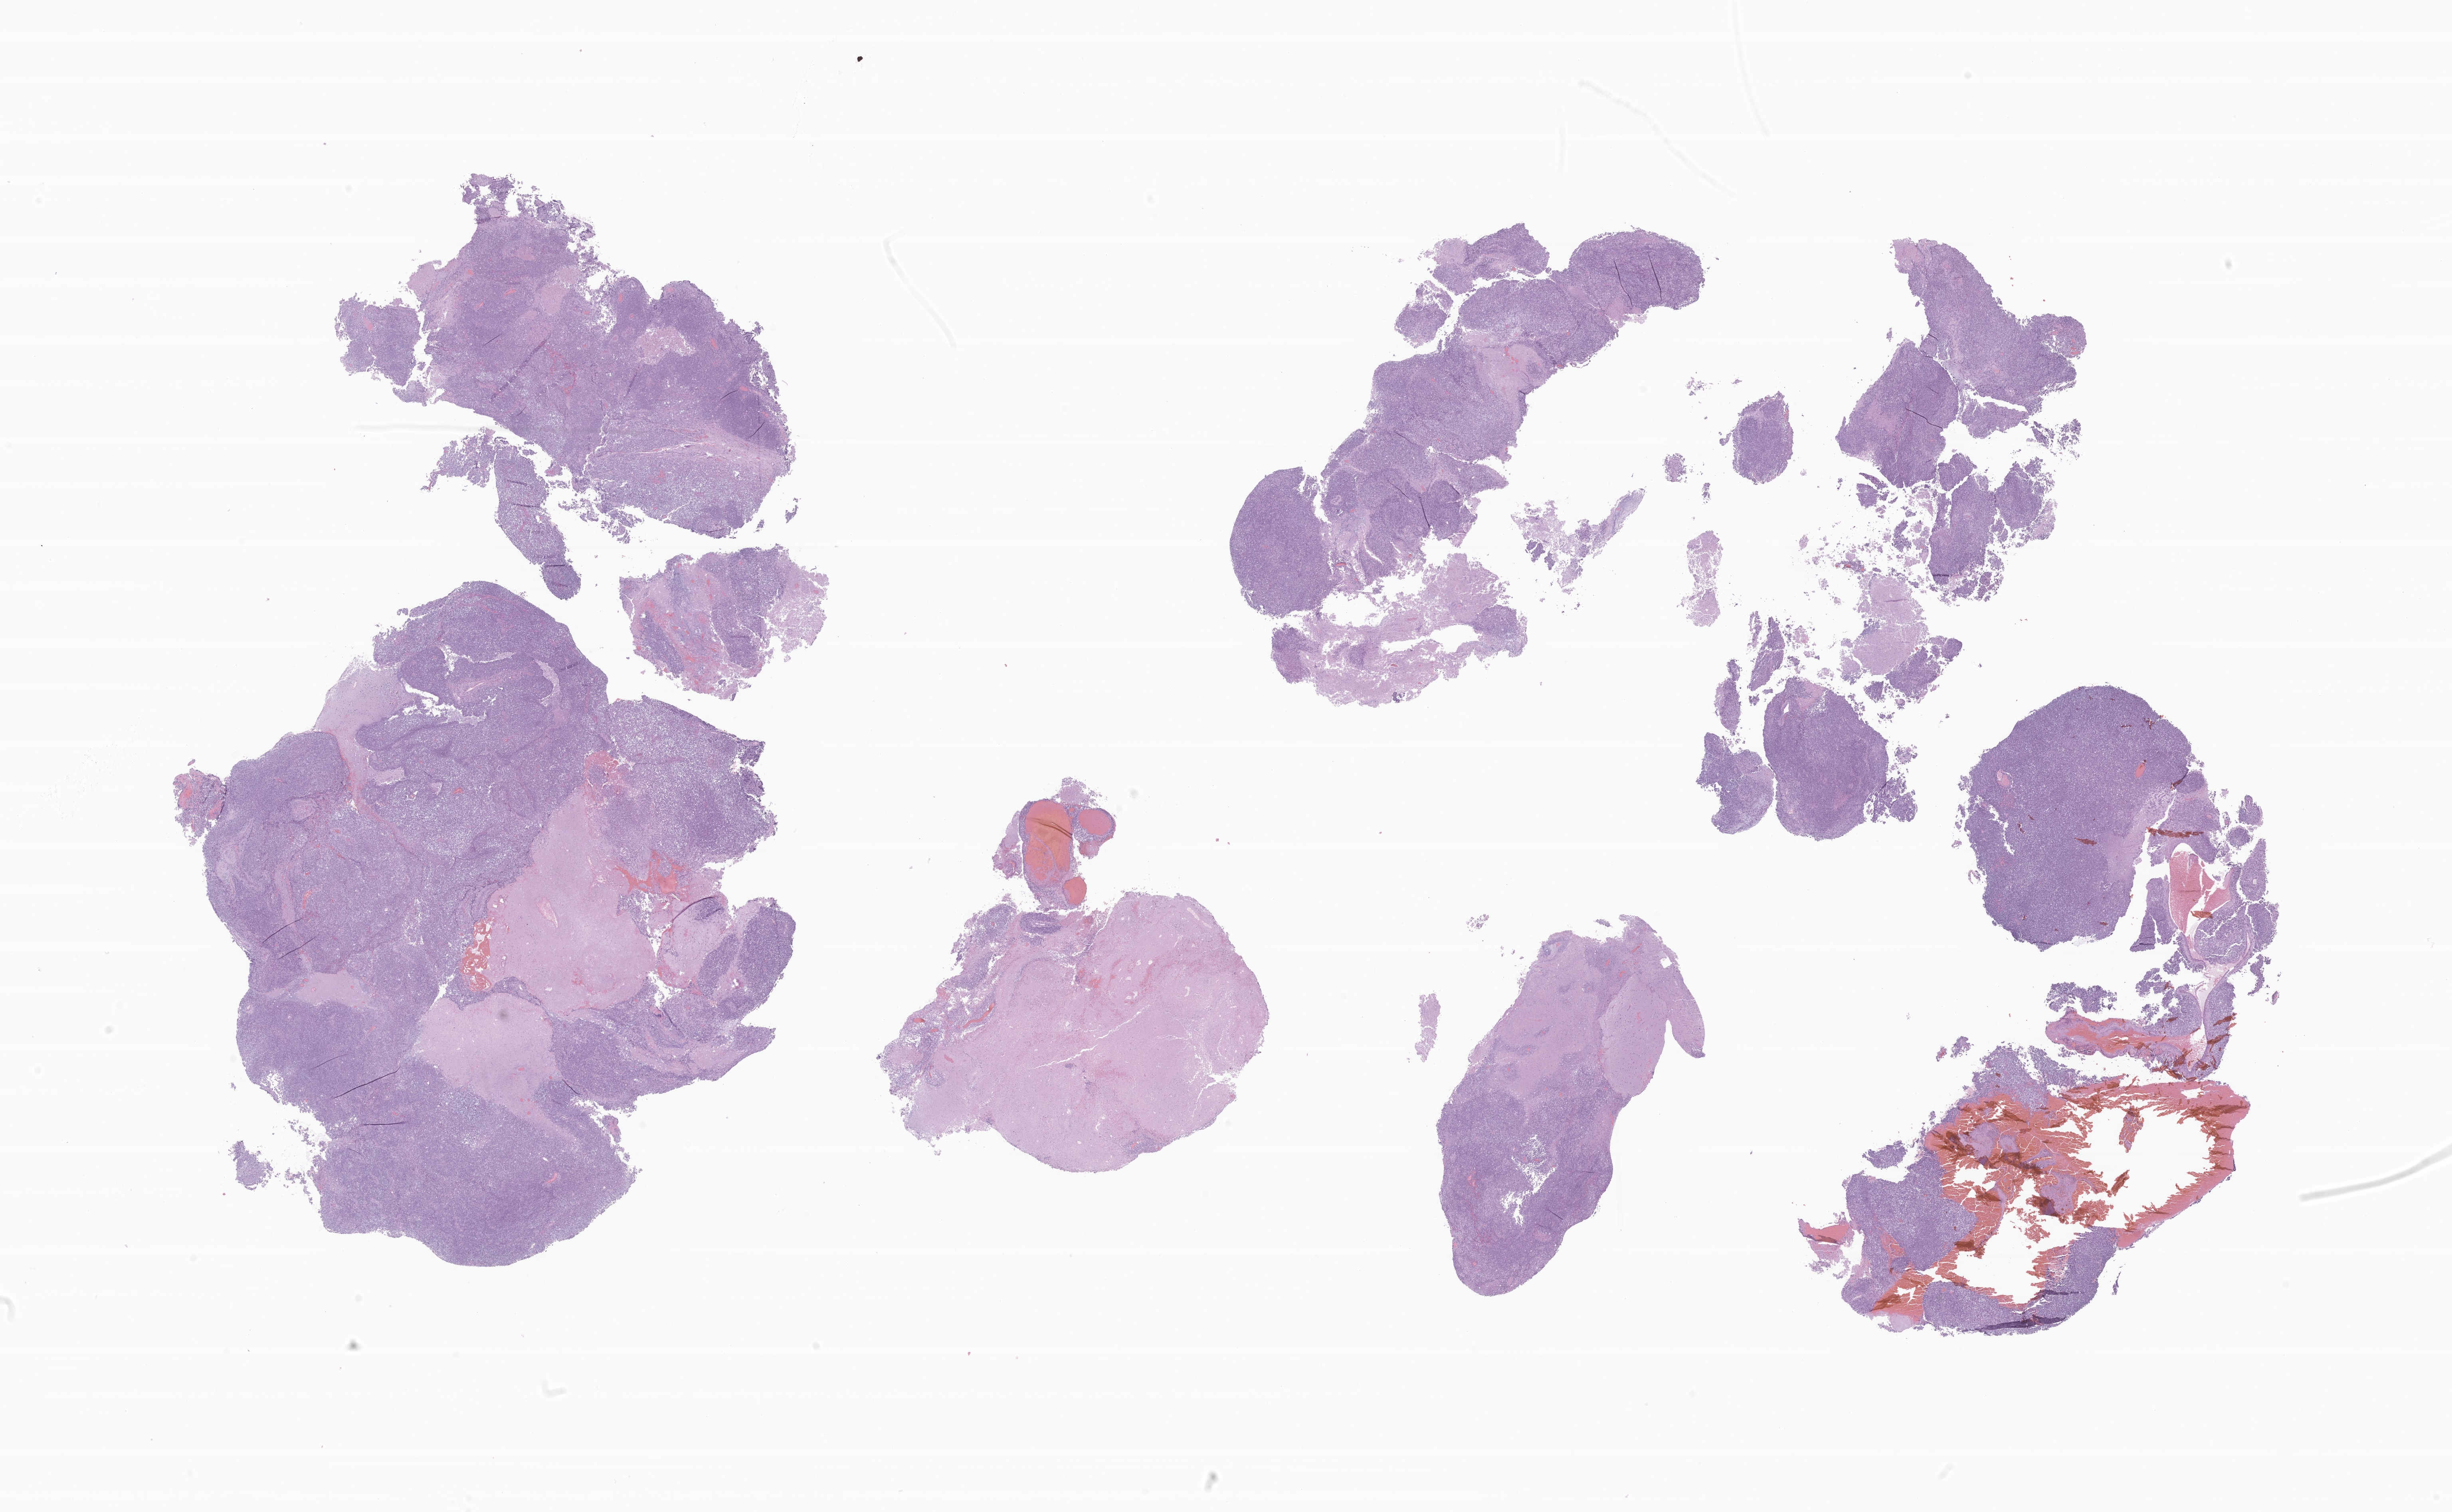
Hematoxylin and eosin (H&E) whole-slide image of tumor tissue from the brain, shown as a low-resolution overview of the whole scanned area (about 25.9 x 16.0 mm), FFPE section. Patient: male, age 40 months (3 years 4 months).
Diagnosis: Atypical teratoid/rhabdoid tumor.